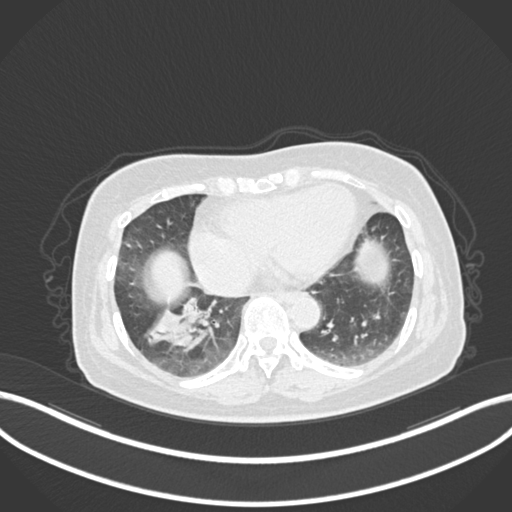
Chest CT, one axial slice. Slice 38 of 222 in the series (ordered by position). Reconstruction kernel B30f. 120 kVp. Lung window (W 1500 / L -600 HU). 1 mm slice thickness. 512 × 512 image matrix. Patient: female, 67 years. From the clinical record (not read from this slice): clinical TNM (as recorded): T1c N1 M0.
Outlined on this slice (rectangle marked by the reading radiologist):
- lung tumour (recorded histology: adenocarcinoma): bounding box [x1, y1, x2, y2] px = [137, 294, 212, 356]